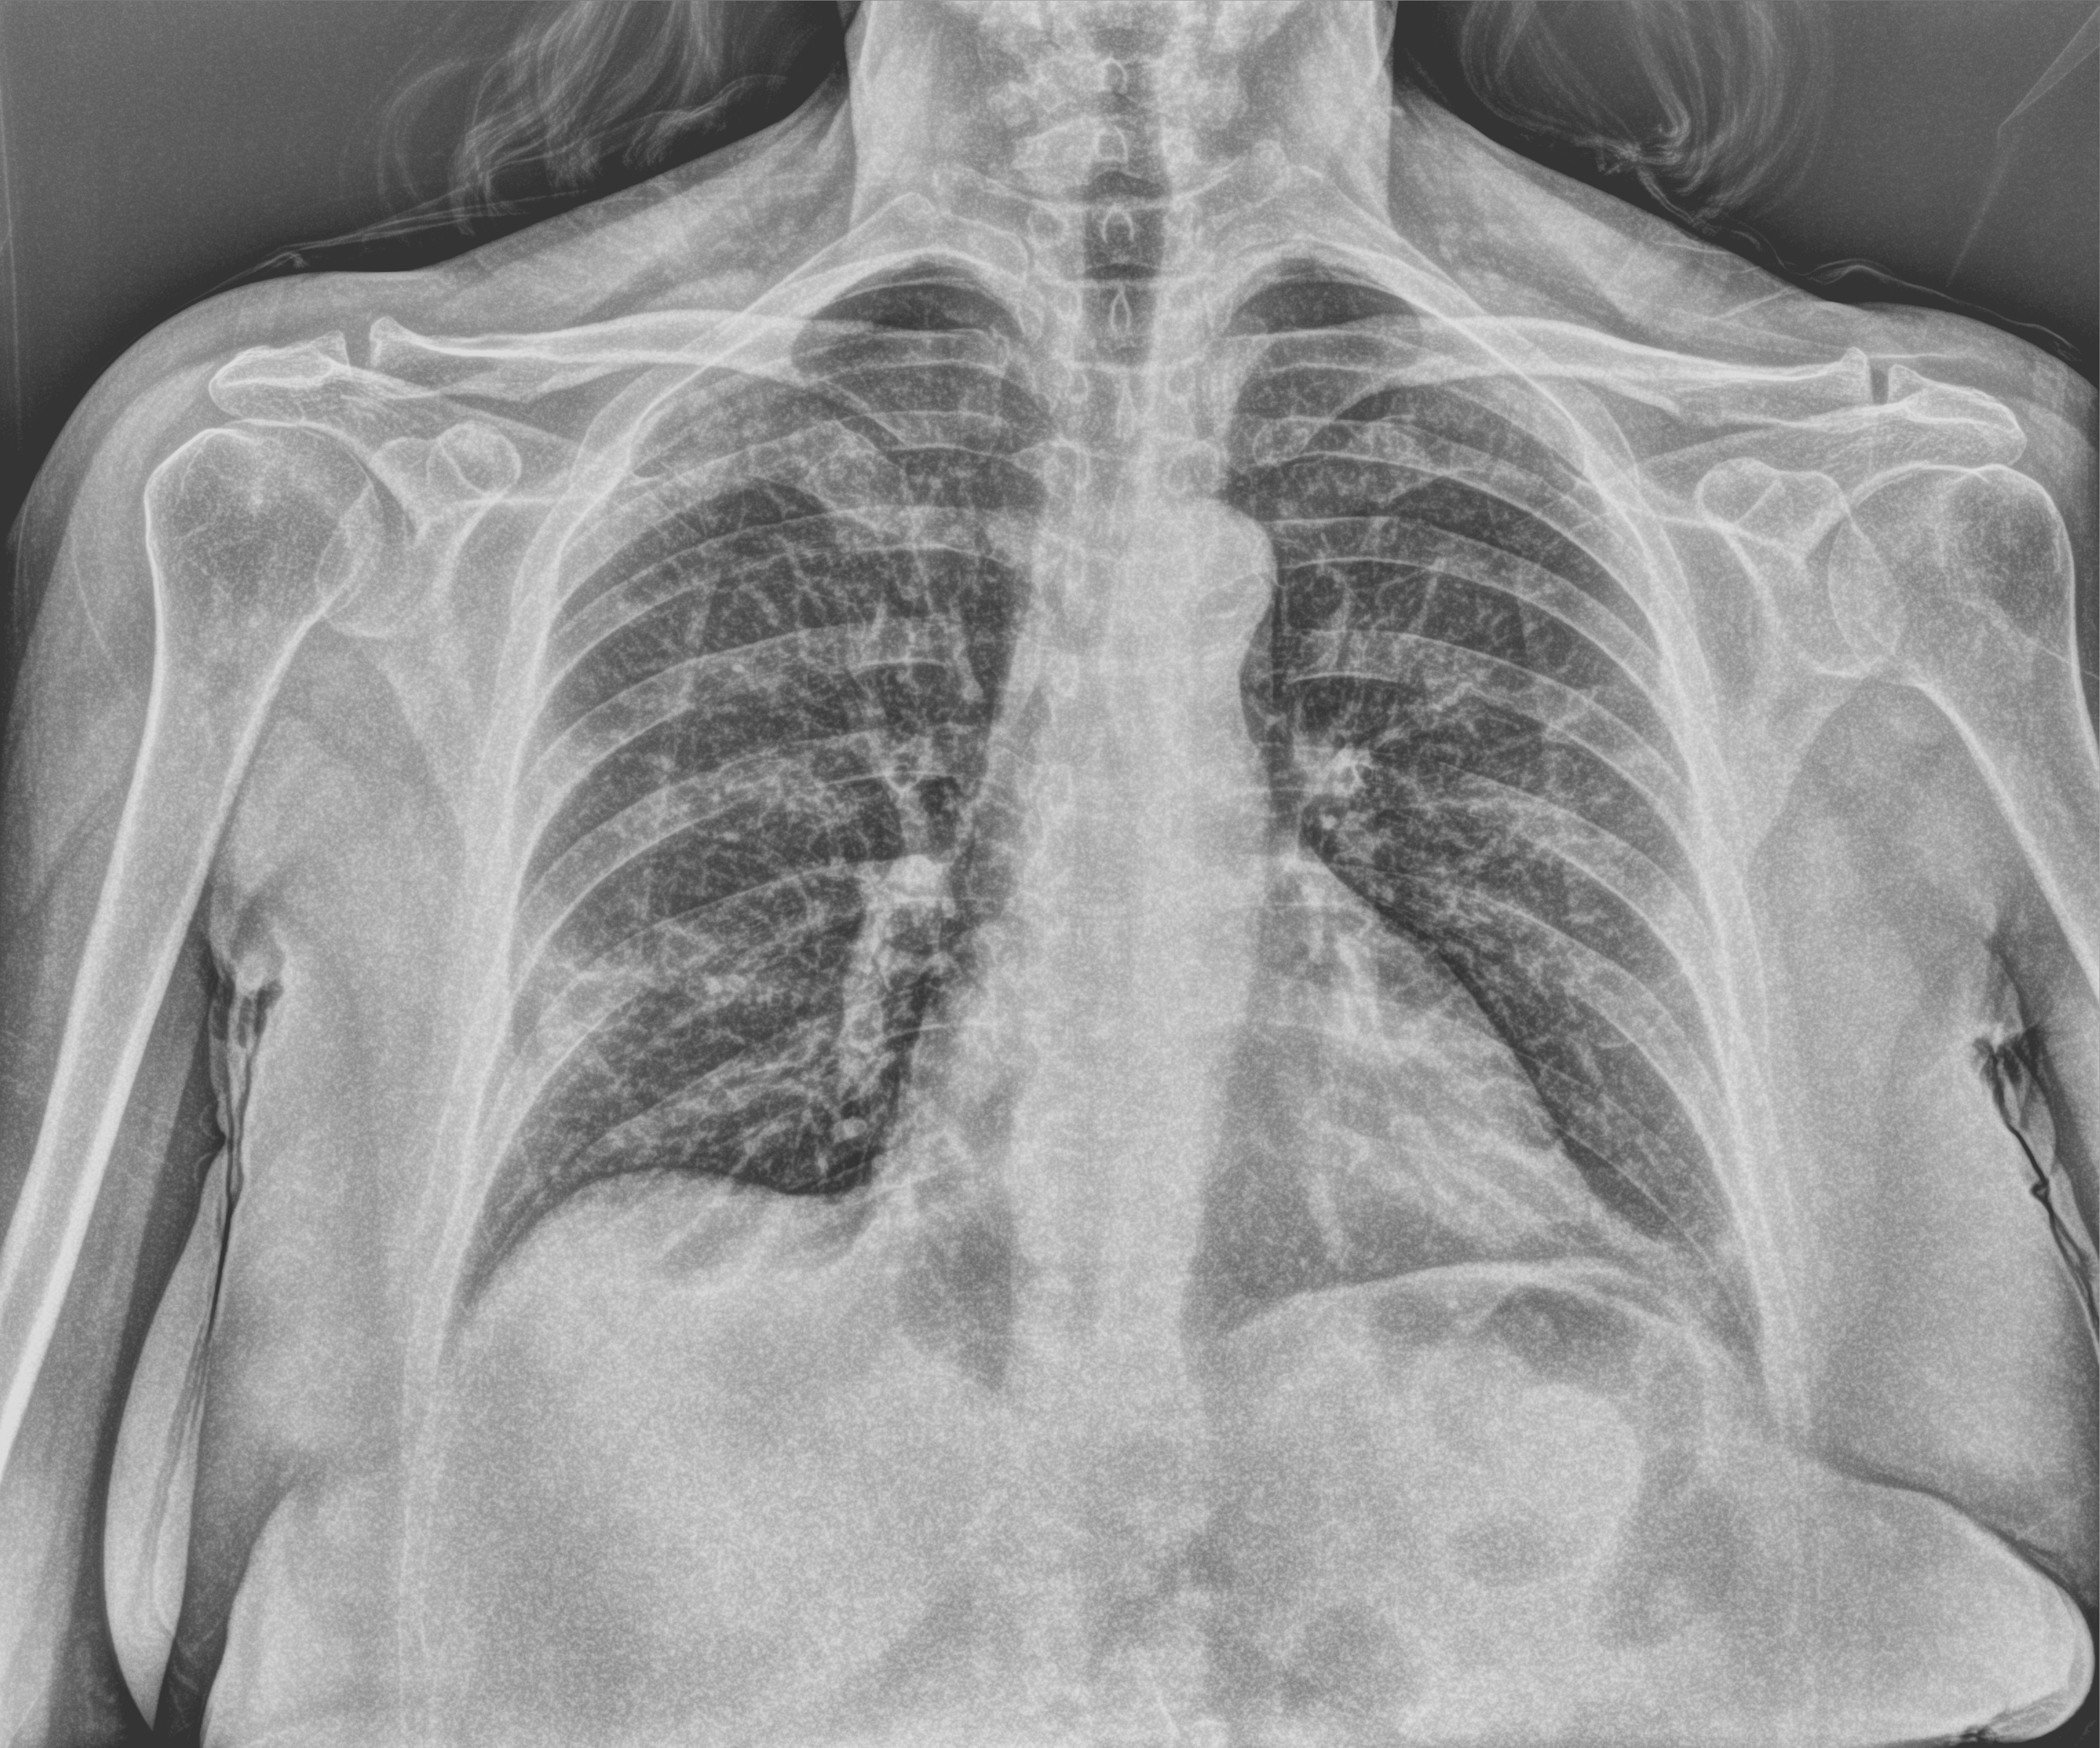
Chest X-ray (portable). Patient hospitalised with COVID-19; female, aged 60–74 years.
From the hospital-stay record, not from the radiograph (when in the stay this image was taken is not recorded): other chronic lung disease (admission record): no; mechanically ventilated during this hospital stay: no.